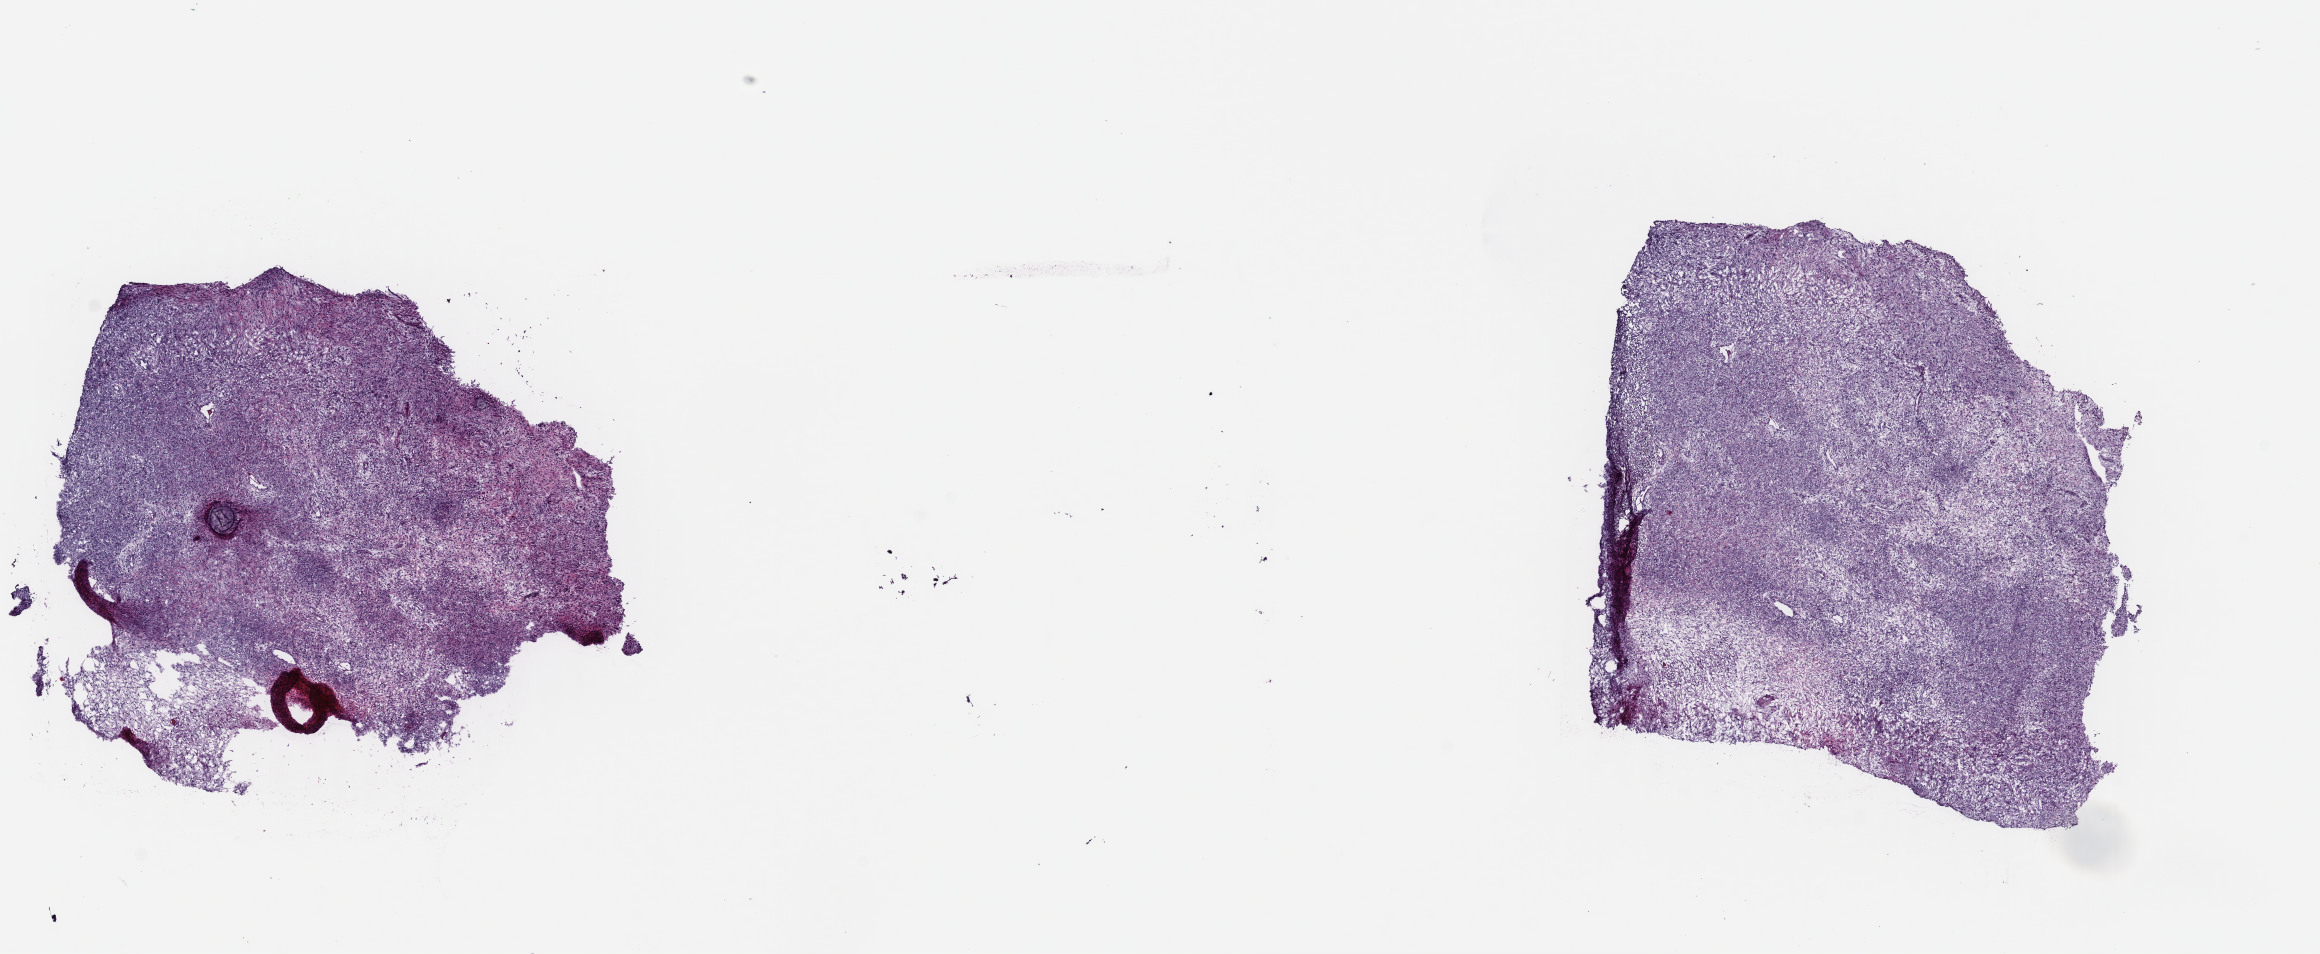
Digitized Hematoxylin and eosin (H&E) stained tissue section (whole slide) — whole scanned area (about 18.3 x 7.5 mm, from a 40x scan) shown as a low-resolution overview; frozen section from the top of the tissue portion; primary tumour sample from the retroperitoneum and peritoneum. Male, age 82 years at initial diagnosis. Composition of this section per pathologist review: tumour cells 90%, tumour nuclei 90%, normal cells 0%, stromal cells 10%, necrosis 0%. Infiltration values recorded for this section: lymphocyte infiltration 0%, monocyte infiltration 0%, neutrophil infiltration 0%.
Pathologic diagnosis: Dedifferentiated liposarcoma (retroperitoneum).